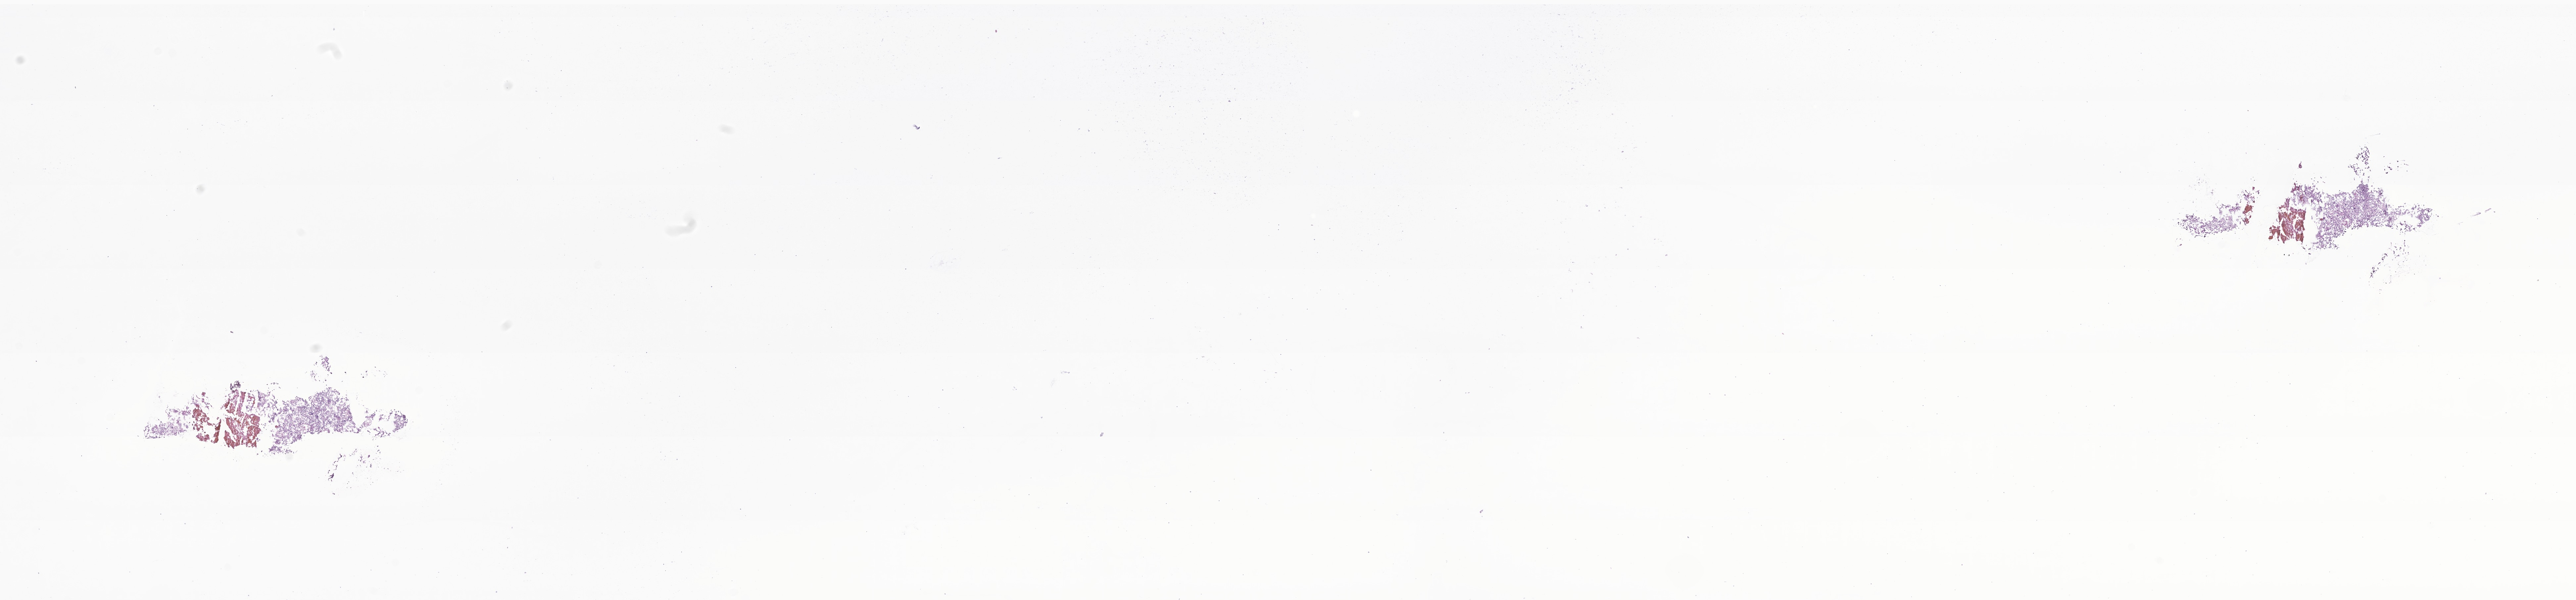
Hematoxylin and eosin (H&E) whole-slide image of tumor tissue from the brain — whole scanned area (about 32.8 x 7.6 mm) shown as a low-resolution overview. Frozen section (OCT-embedded). Patient female; age 106 months (8 years 10 months).
Diagnosis: Neoplasm, uncertain whether benign or malignant.